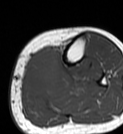
MRI of an extremity soft-tissue mass, one axial slice; position 21 of 68 along the scan axis; MR volume resampled by the dataset authors to the PET/CT grid (not the native acquisition matrix); 123 × 134 image matrix, field of view 120 × 131 mm. Female patient. Case-level facts recorded for this patient, not image findings: histological type: extraskeletal high grade osteogenic sarcoma; grade: high; site of the primary tumour: left calf.
Outlined on this slice (expert contour drawn on MRI and transferred to this co-registered scan by the dataset authors):
- gross tumour volume (mass): box from (x=24, y=48) to (x=59, y=95) px